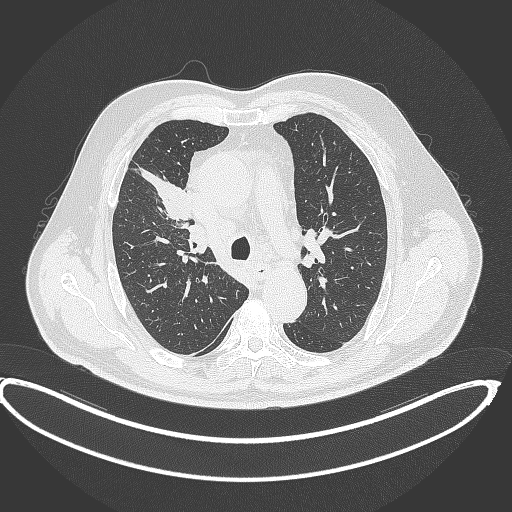
Chest CT, one axial slice; slice 279 of 390 in the series (ordered by position); reconstruction kernel B70f; lung window (W 1500 / L -600 HU); 1 mm slice thickness; 512 × 512 image matrix. Male patient, age 62 years. Case-level facts recorded for this patient, not image findings: clinical TNM (as recorded): T1c N3 M1c.
Annotated regions visible in this slice (bounding box drawn by a radiologist):
- lung tumour (recorded histology: adenocarcinoma): bounding box <138,168,193,221> (left, top, right, bottom; pixels)